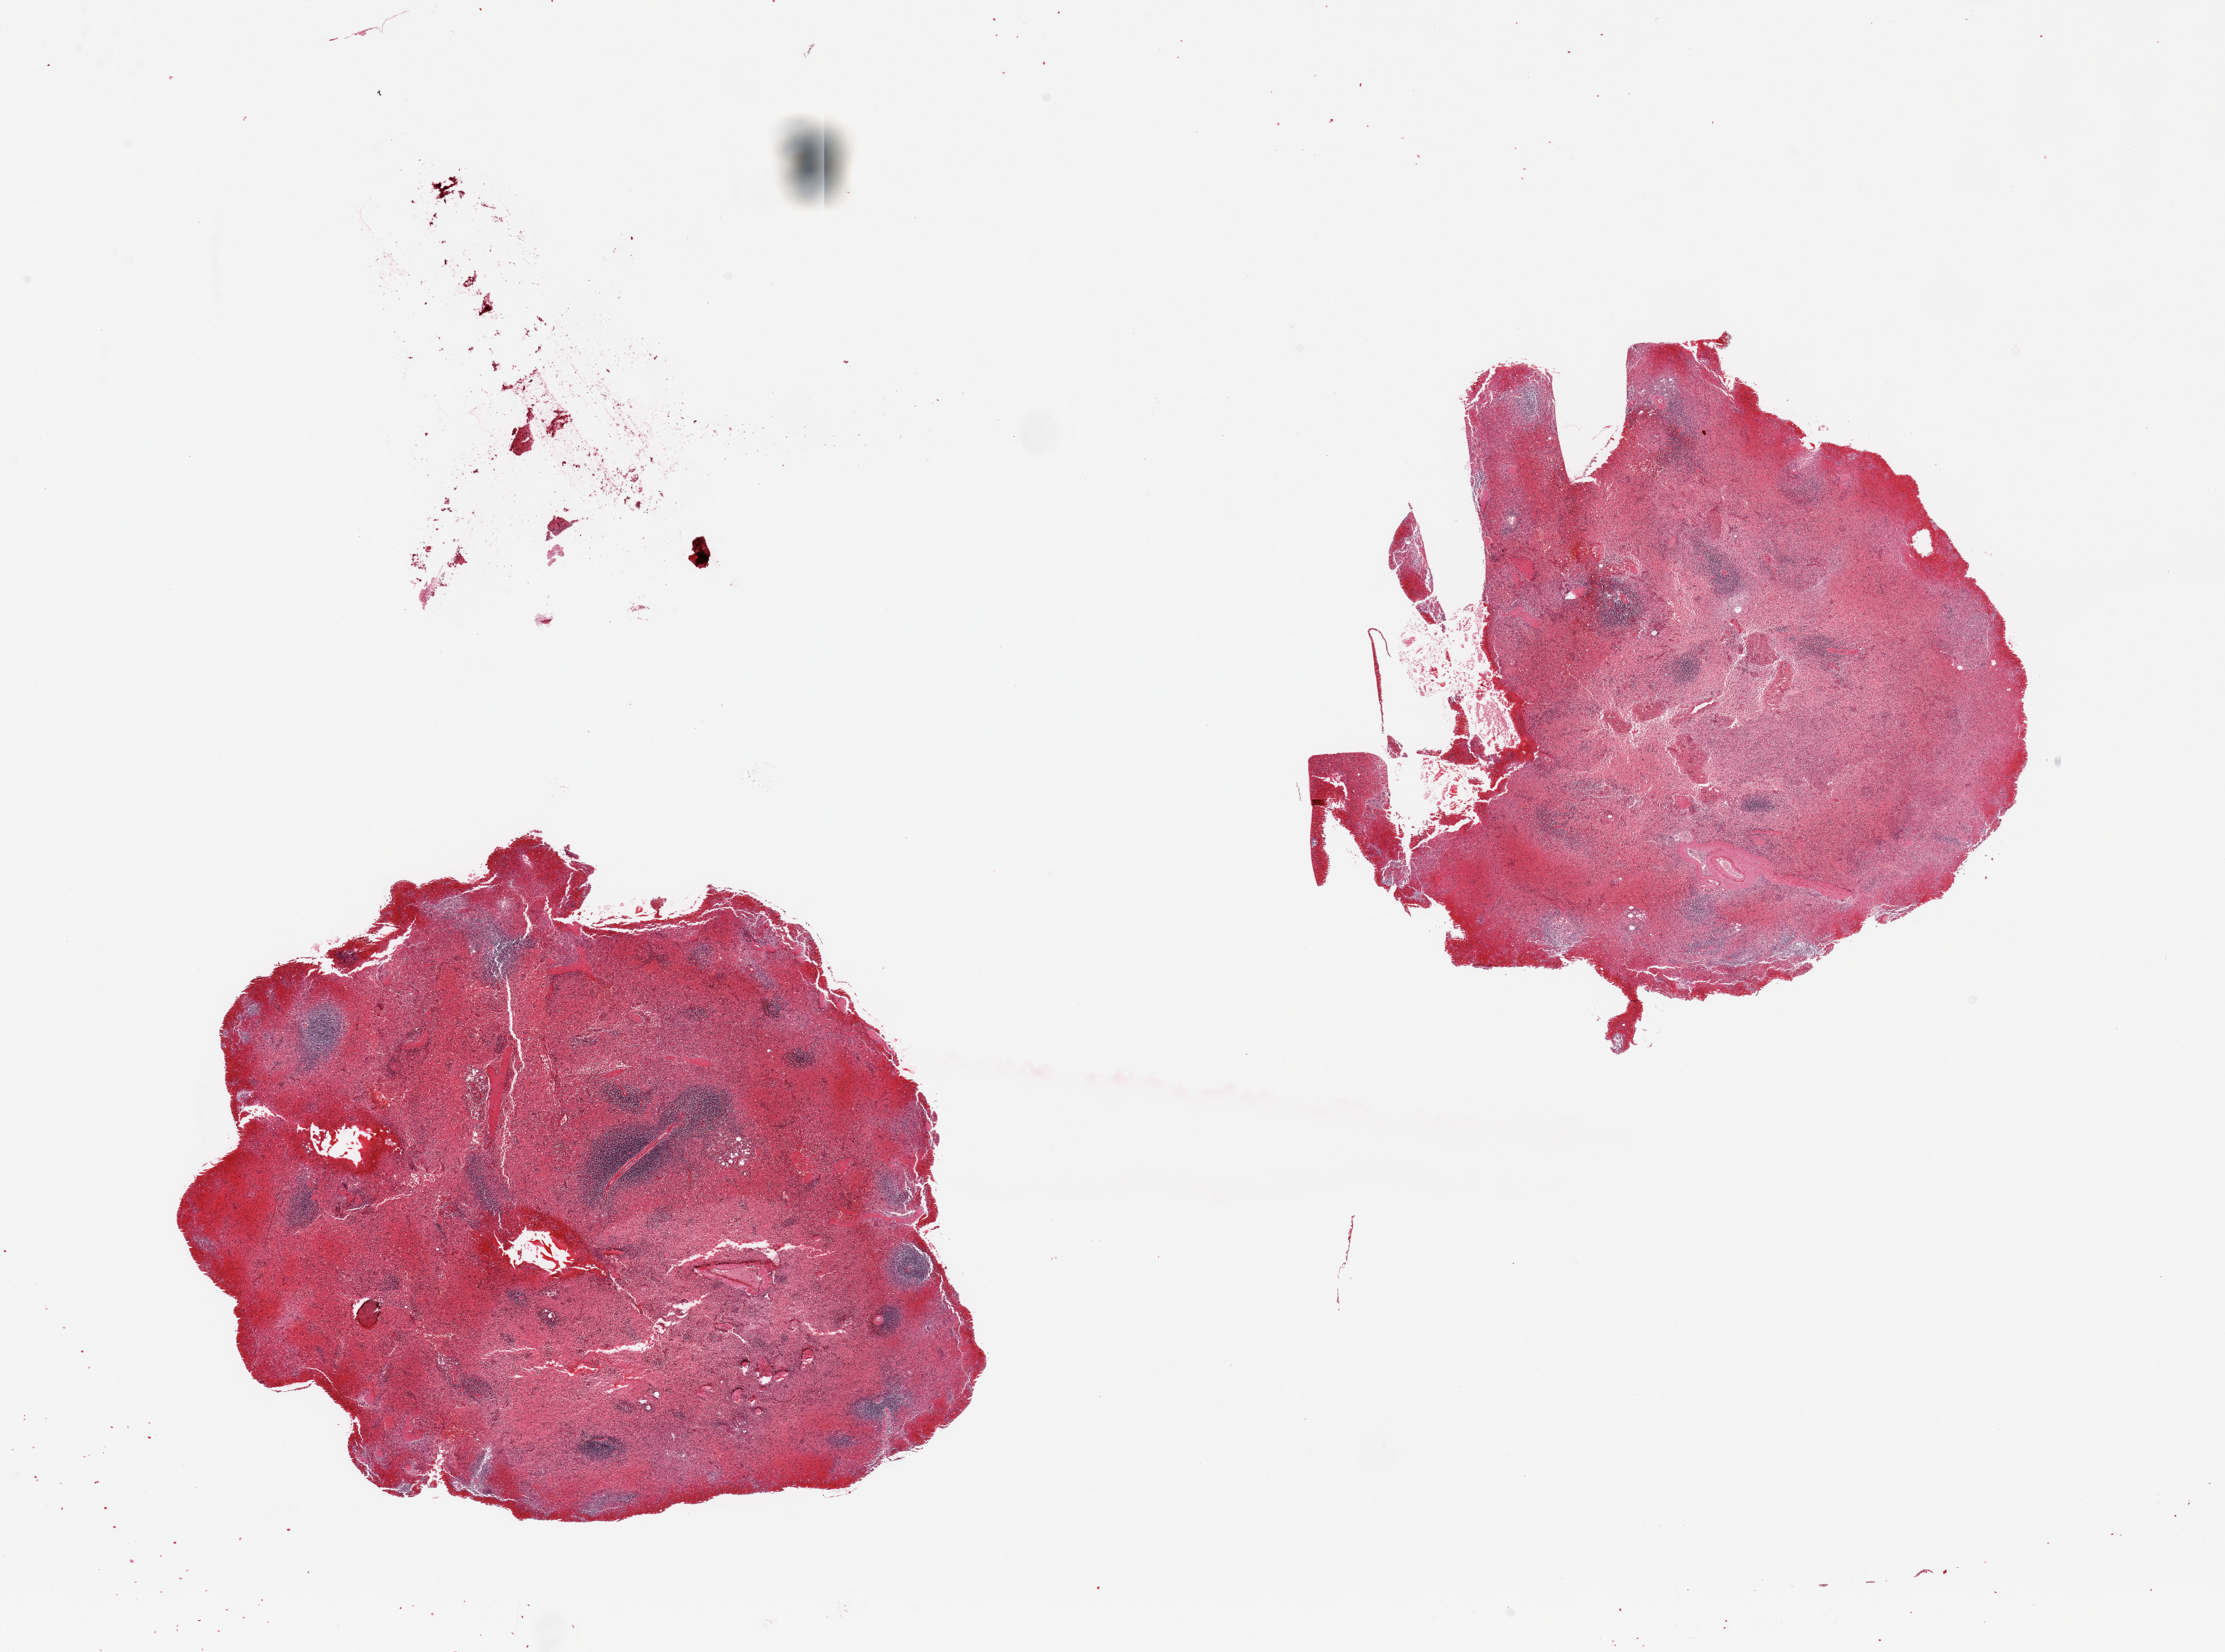
Hematoxylin and eosin (H&E) whole-slide image, low-resolution overview of the scanned area, about 26.6 x 19.7 mm. PAXgene-fixed paraffin-embedded (PFPE) section. Target tissue: spleen. Donor tissue sample. Donor sex: male.
Review note (as recorded): 2 pieces, moderate congestion.